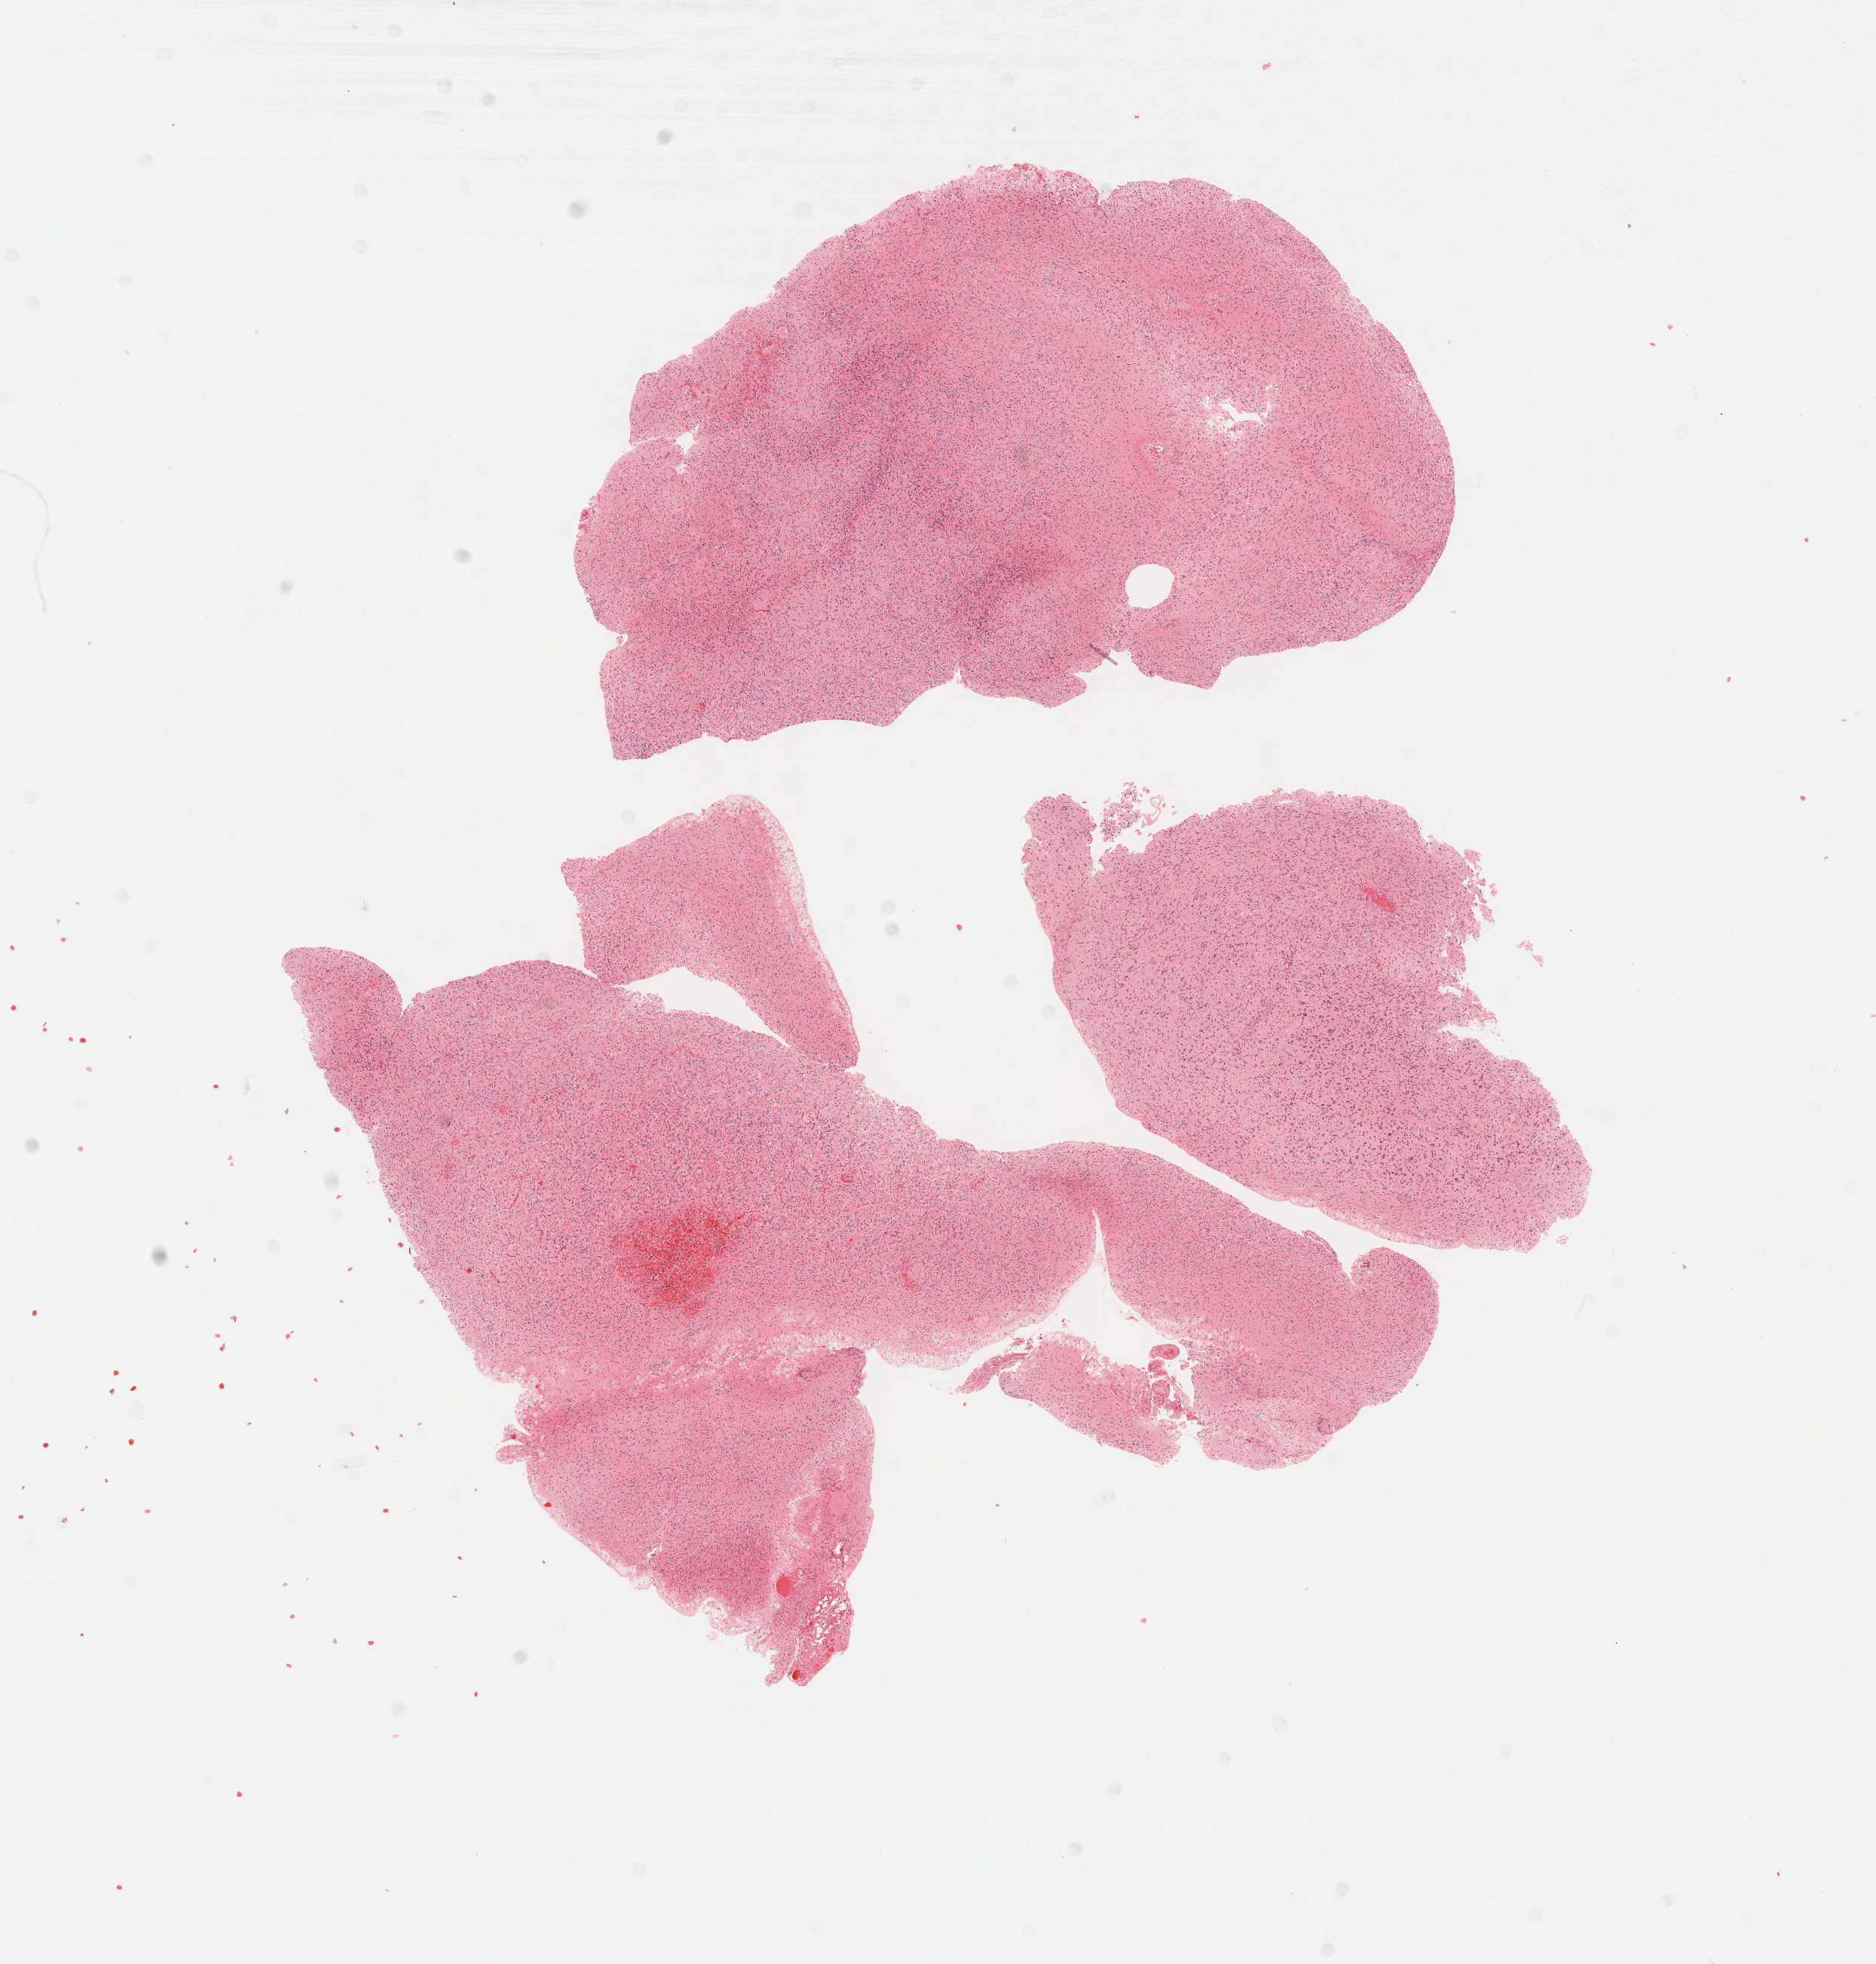
H&E whole-slide image — whole scanned area (about 10.1 x 10.5 mm, from a 40x scan) shown as a low-resolution overview, formalin-fixed paraffin-embedded (FFPE) diagnostic section, primary tumour sample from the brain. Male patient; age at initial diagnosis 69 years. Histologic grade: G3 (poorly differentiated).
Histologic diagnosis: Astrocytoma, anaplastic (cerebrum).